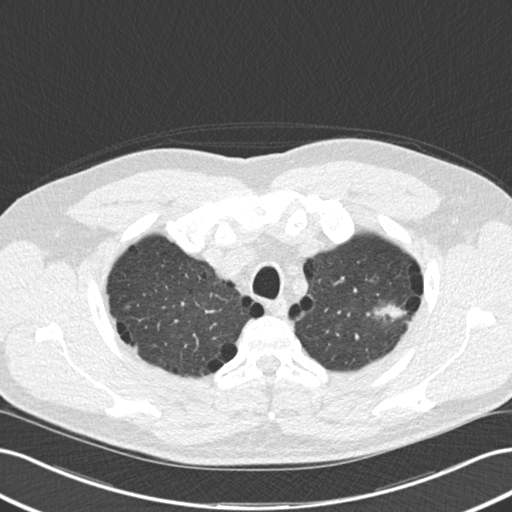
Low-dose screening chest CT, one axial slice. Position 141 of 177 along the scan axis. Reconstruction kernel B30f. Lung window (W 1500 / L -600 HU). 2 mm slice thickness. 512 × 512 image matrix, field of view 360 × 360 mm.
Outlined on this slice (expert manual segmentation):
- lesion 1 (tumor, upper lobe of left lung): bounding box <374,304,406,321> (left, top, right, bottom; pixels)